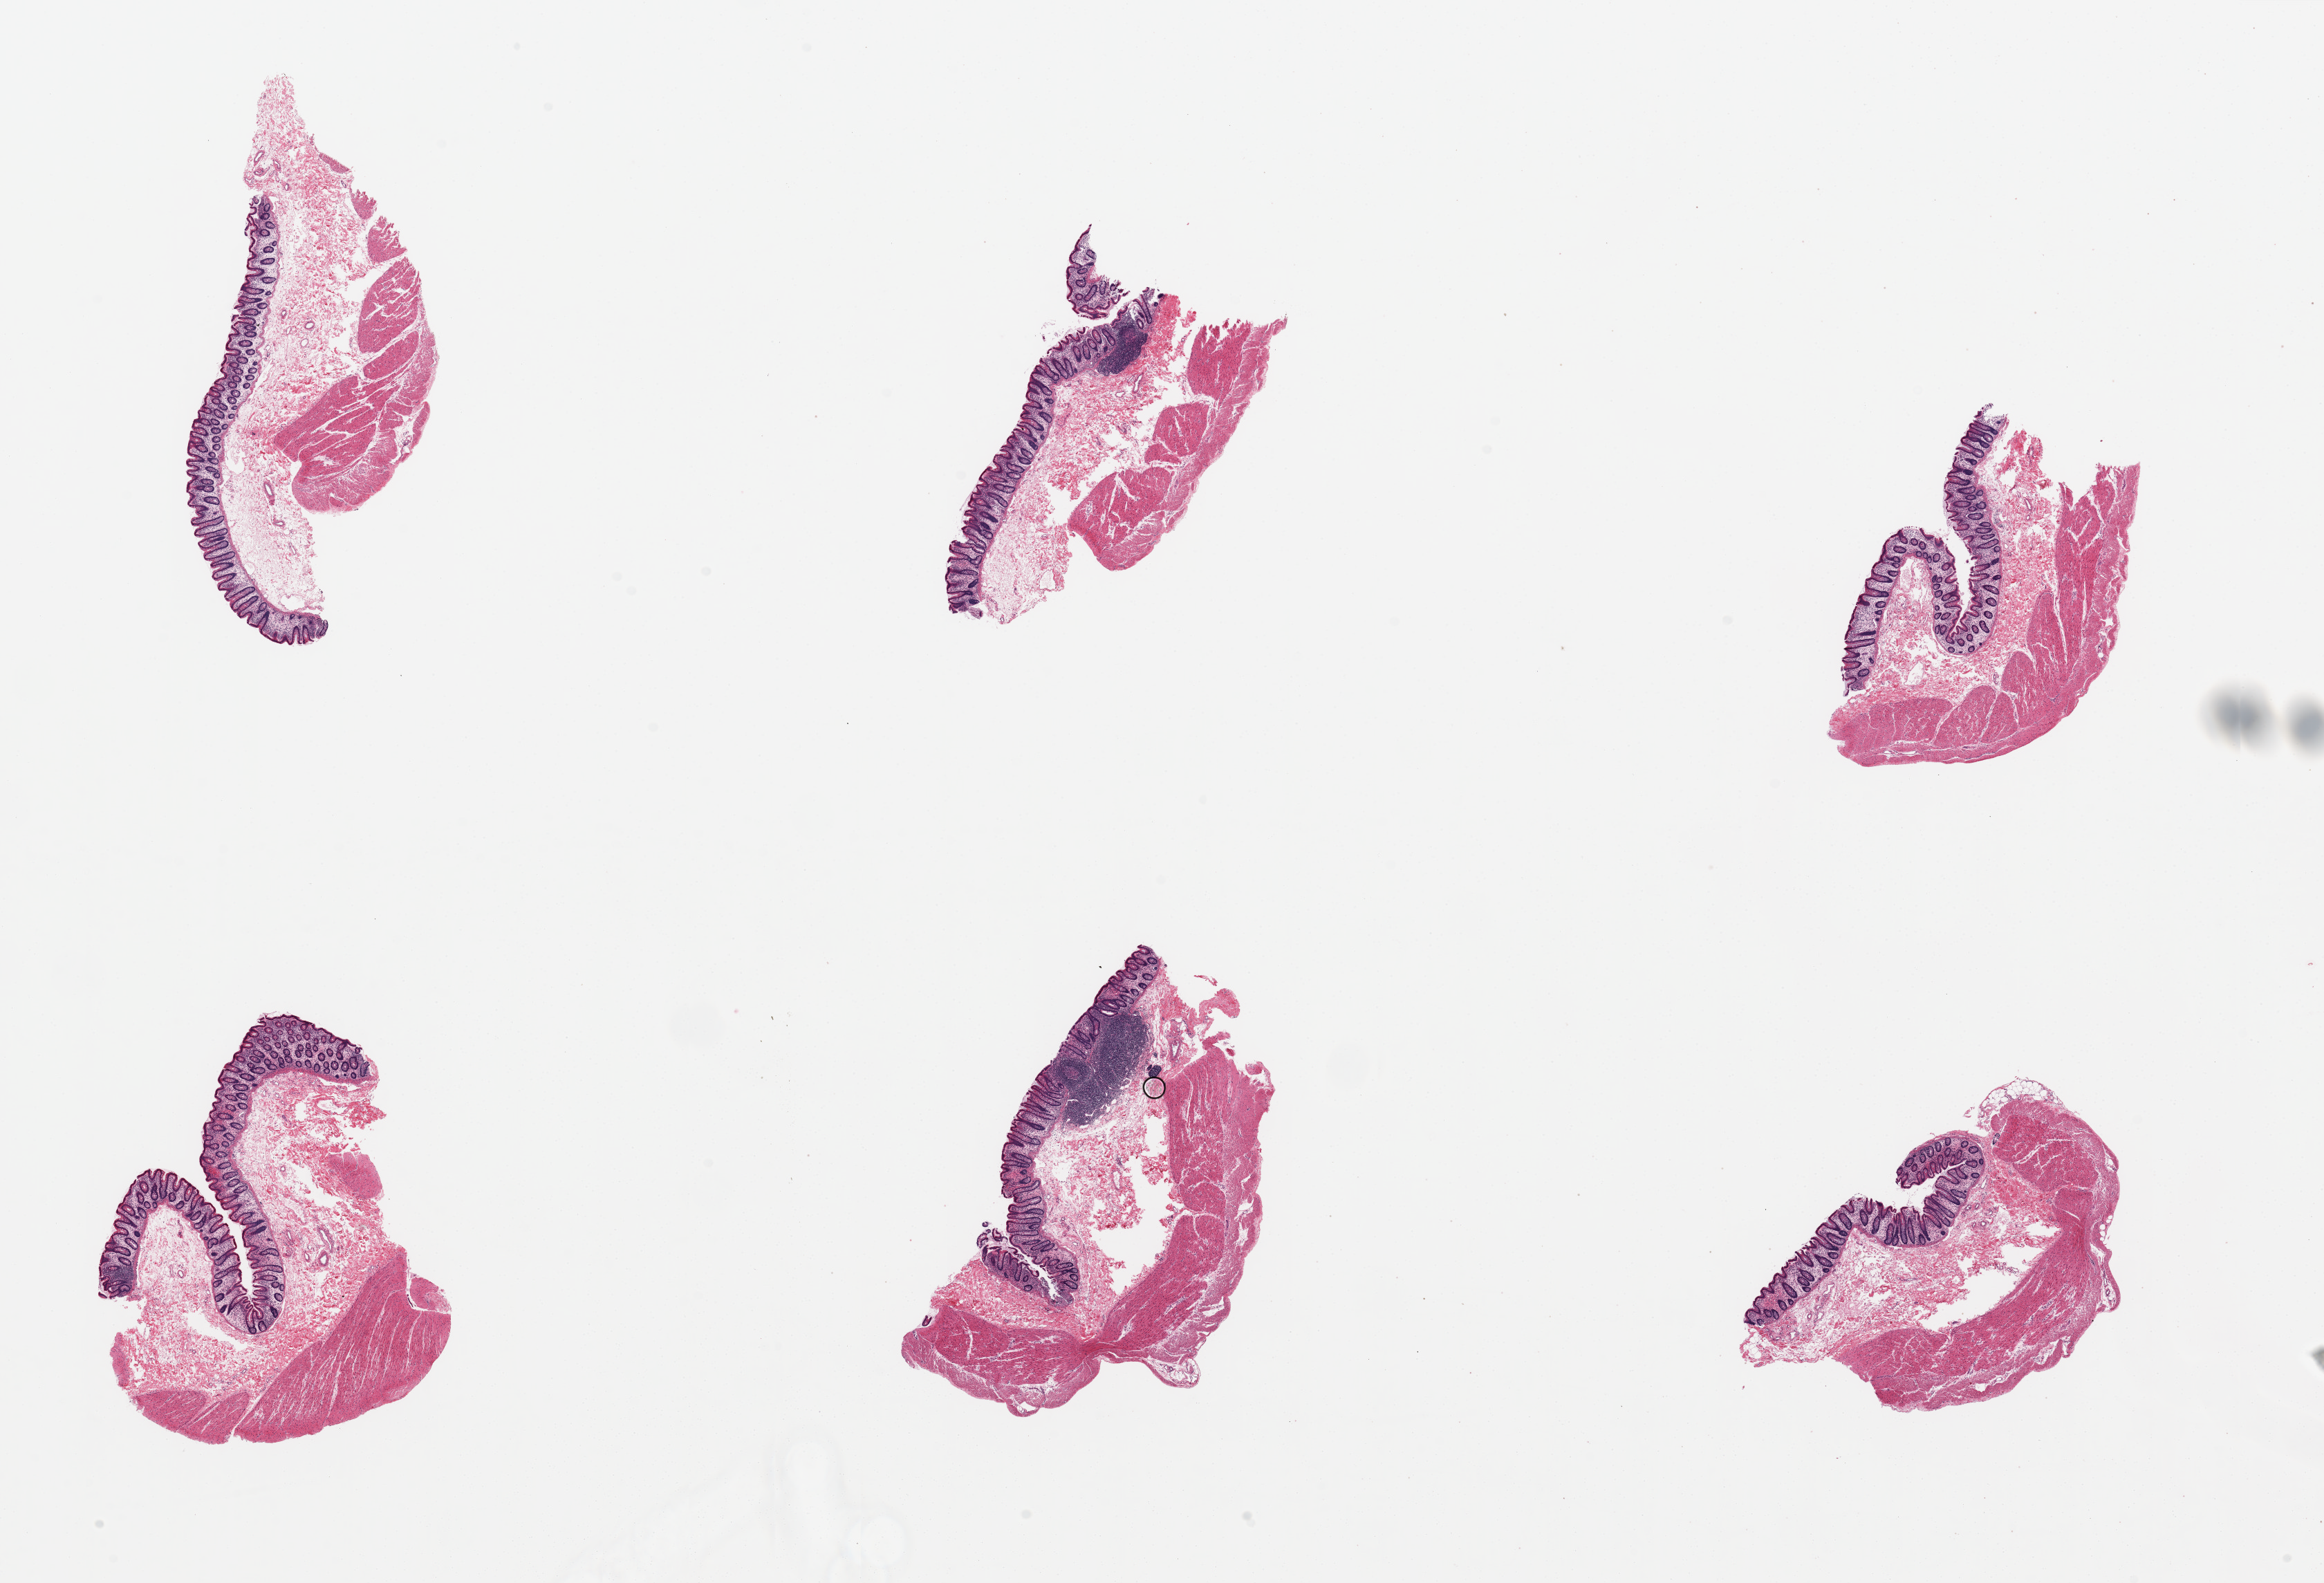
Whole-slide image, H&E stain — low-resolution overview of the scanned area, about 26.6 x 18.1 mm; PAXgene-fixed, paraffin-embedded tissue; section of transverse colon (target tissue); tissue donor sample. Donor: female.
Review note (as recorded): 6 pieces, up to 6x3mm; all have full thickness with good mucosa.